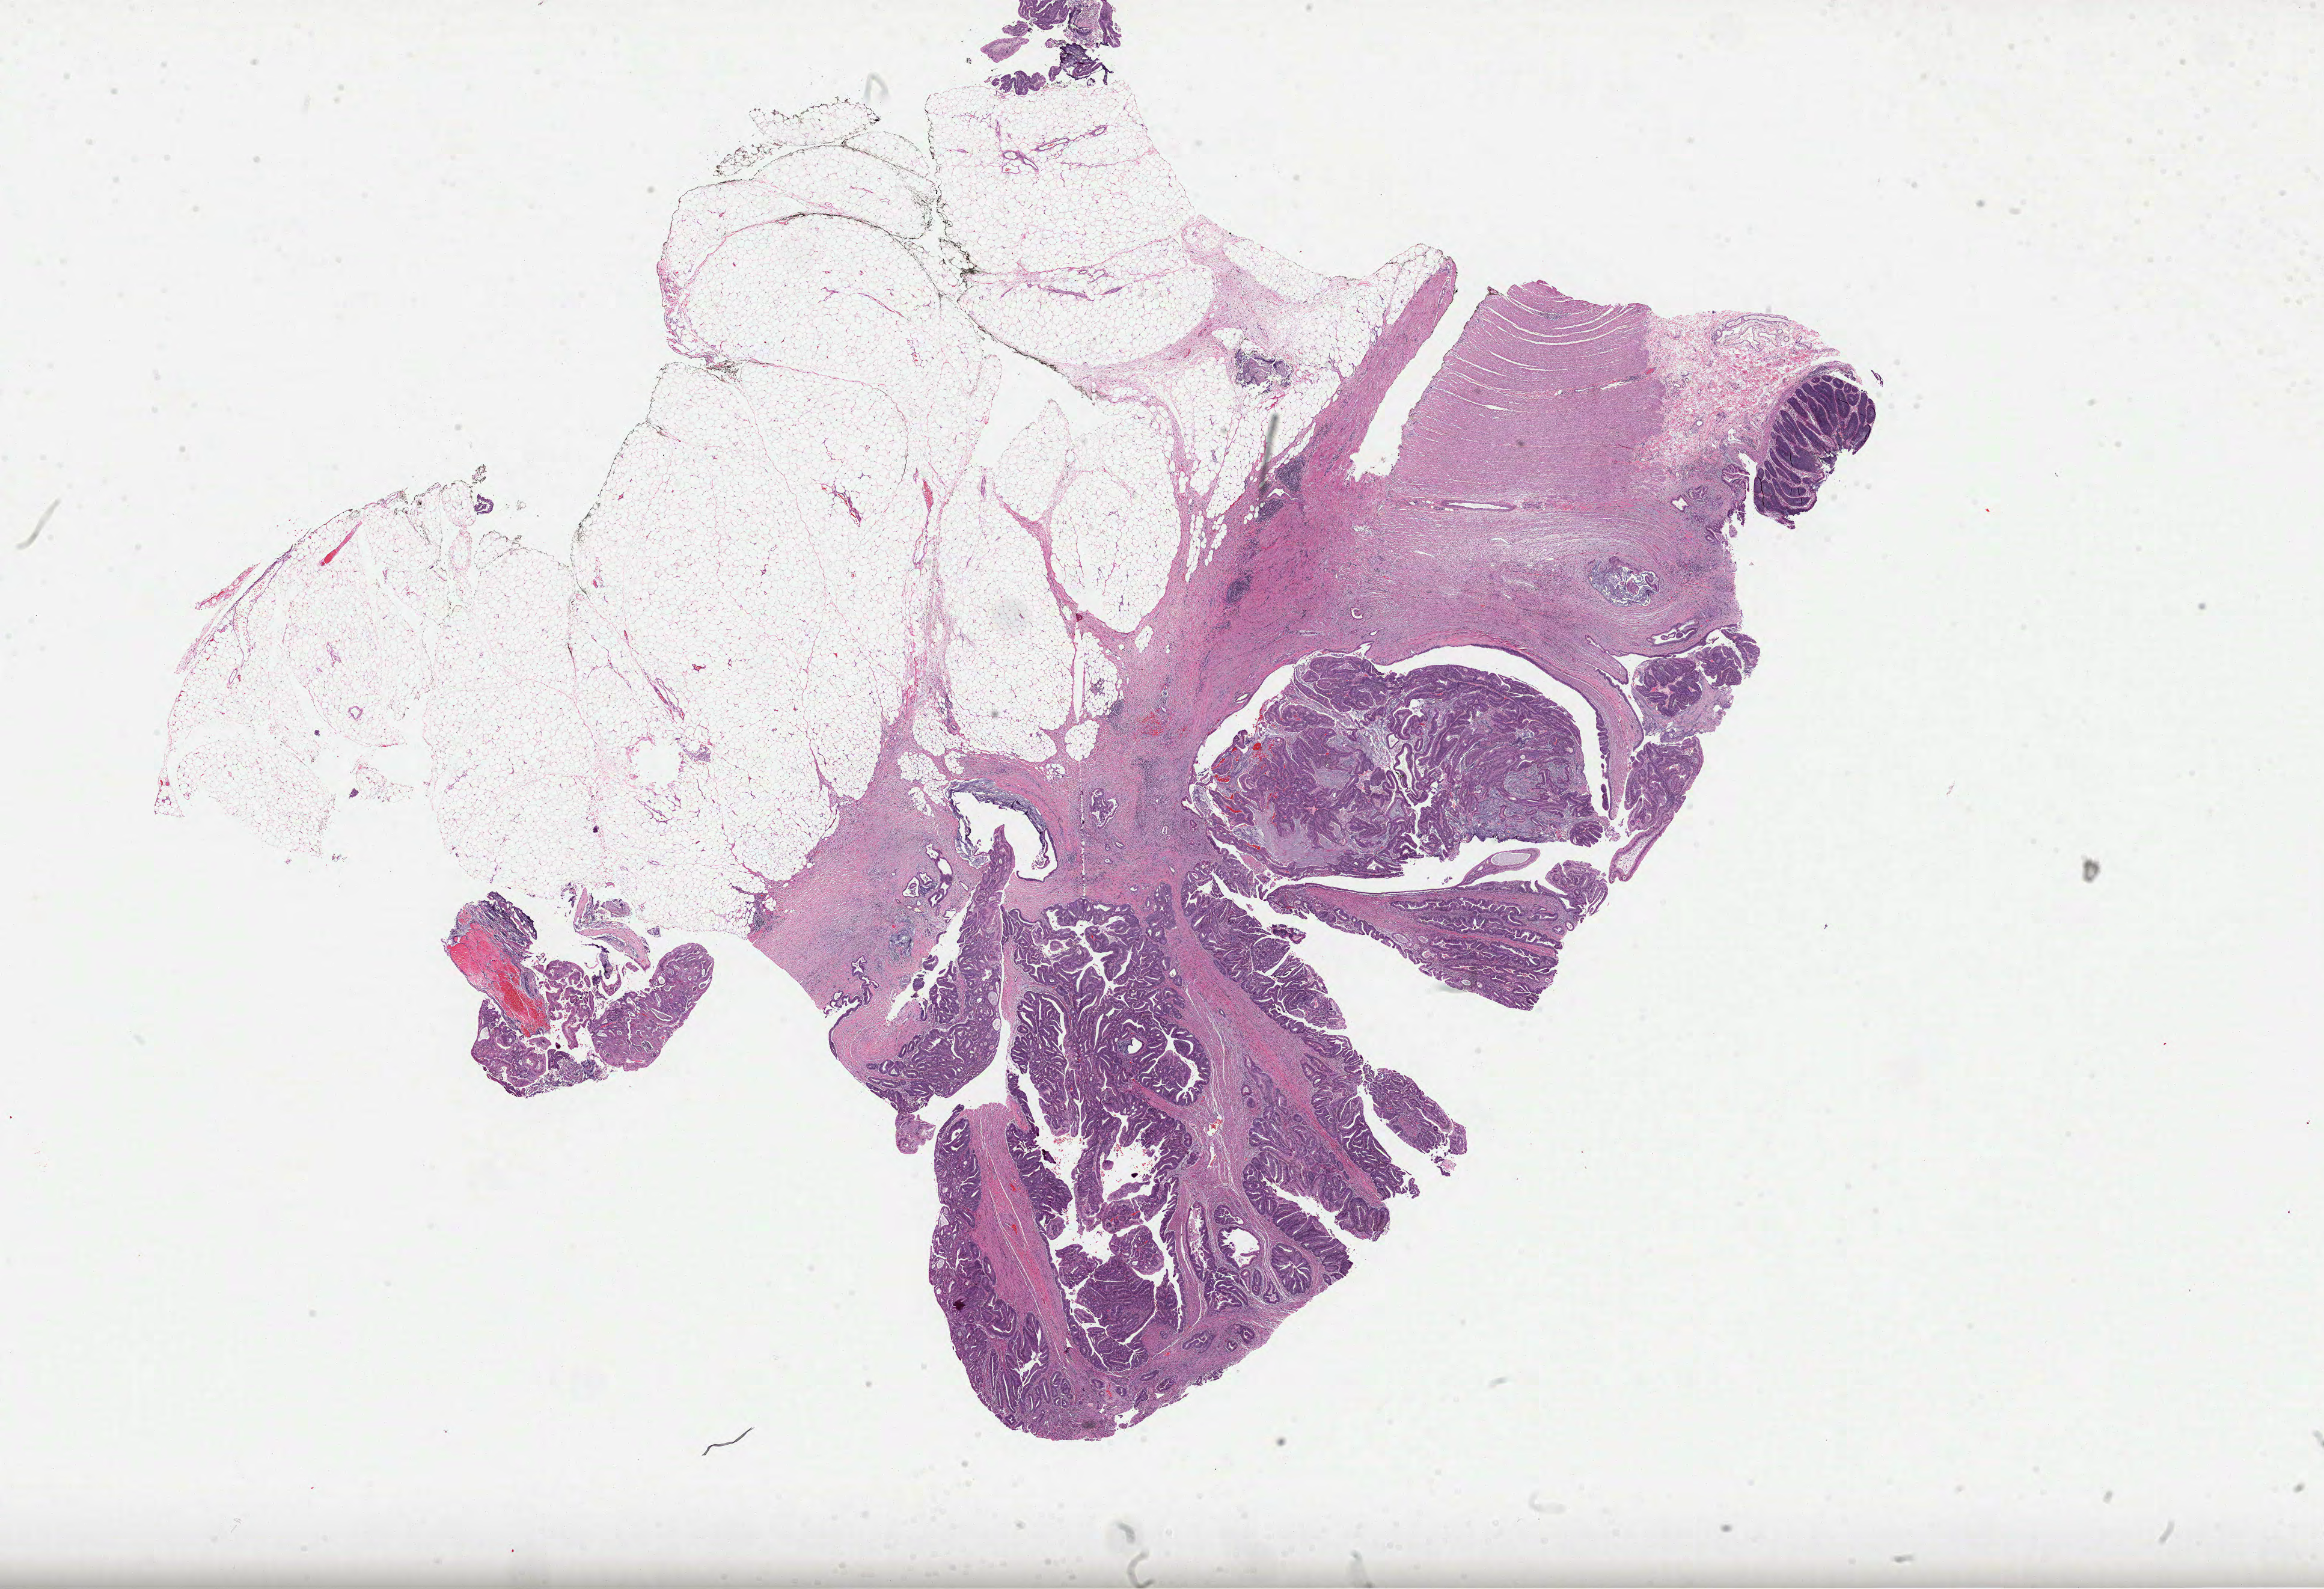
Digitized H&E-stained tissue section (whole slide) — low-resolution overview of the scanned area, about 31.2 x 21.3 mm, formalin-fixed paraffin-embedded (FFPE) diagnostic section, sample: primary tumour, colon. Patient: female, age at initial diagnosis 63 years.
- lymph nodes positive (case pathology): 0 of 19 examined
- histologic diagnosis: Adenocarcinoma, NOS (sigmoid colon)
- AJCC pathologic stage: IVA (7th edition)